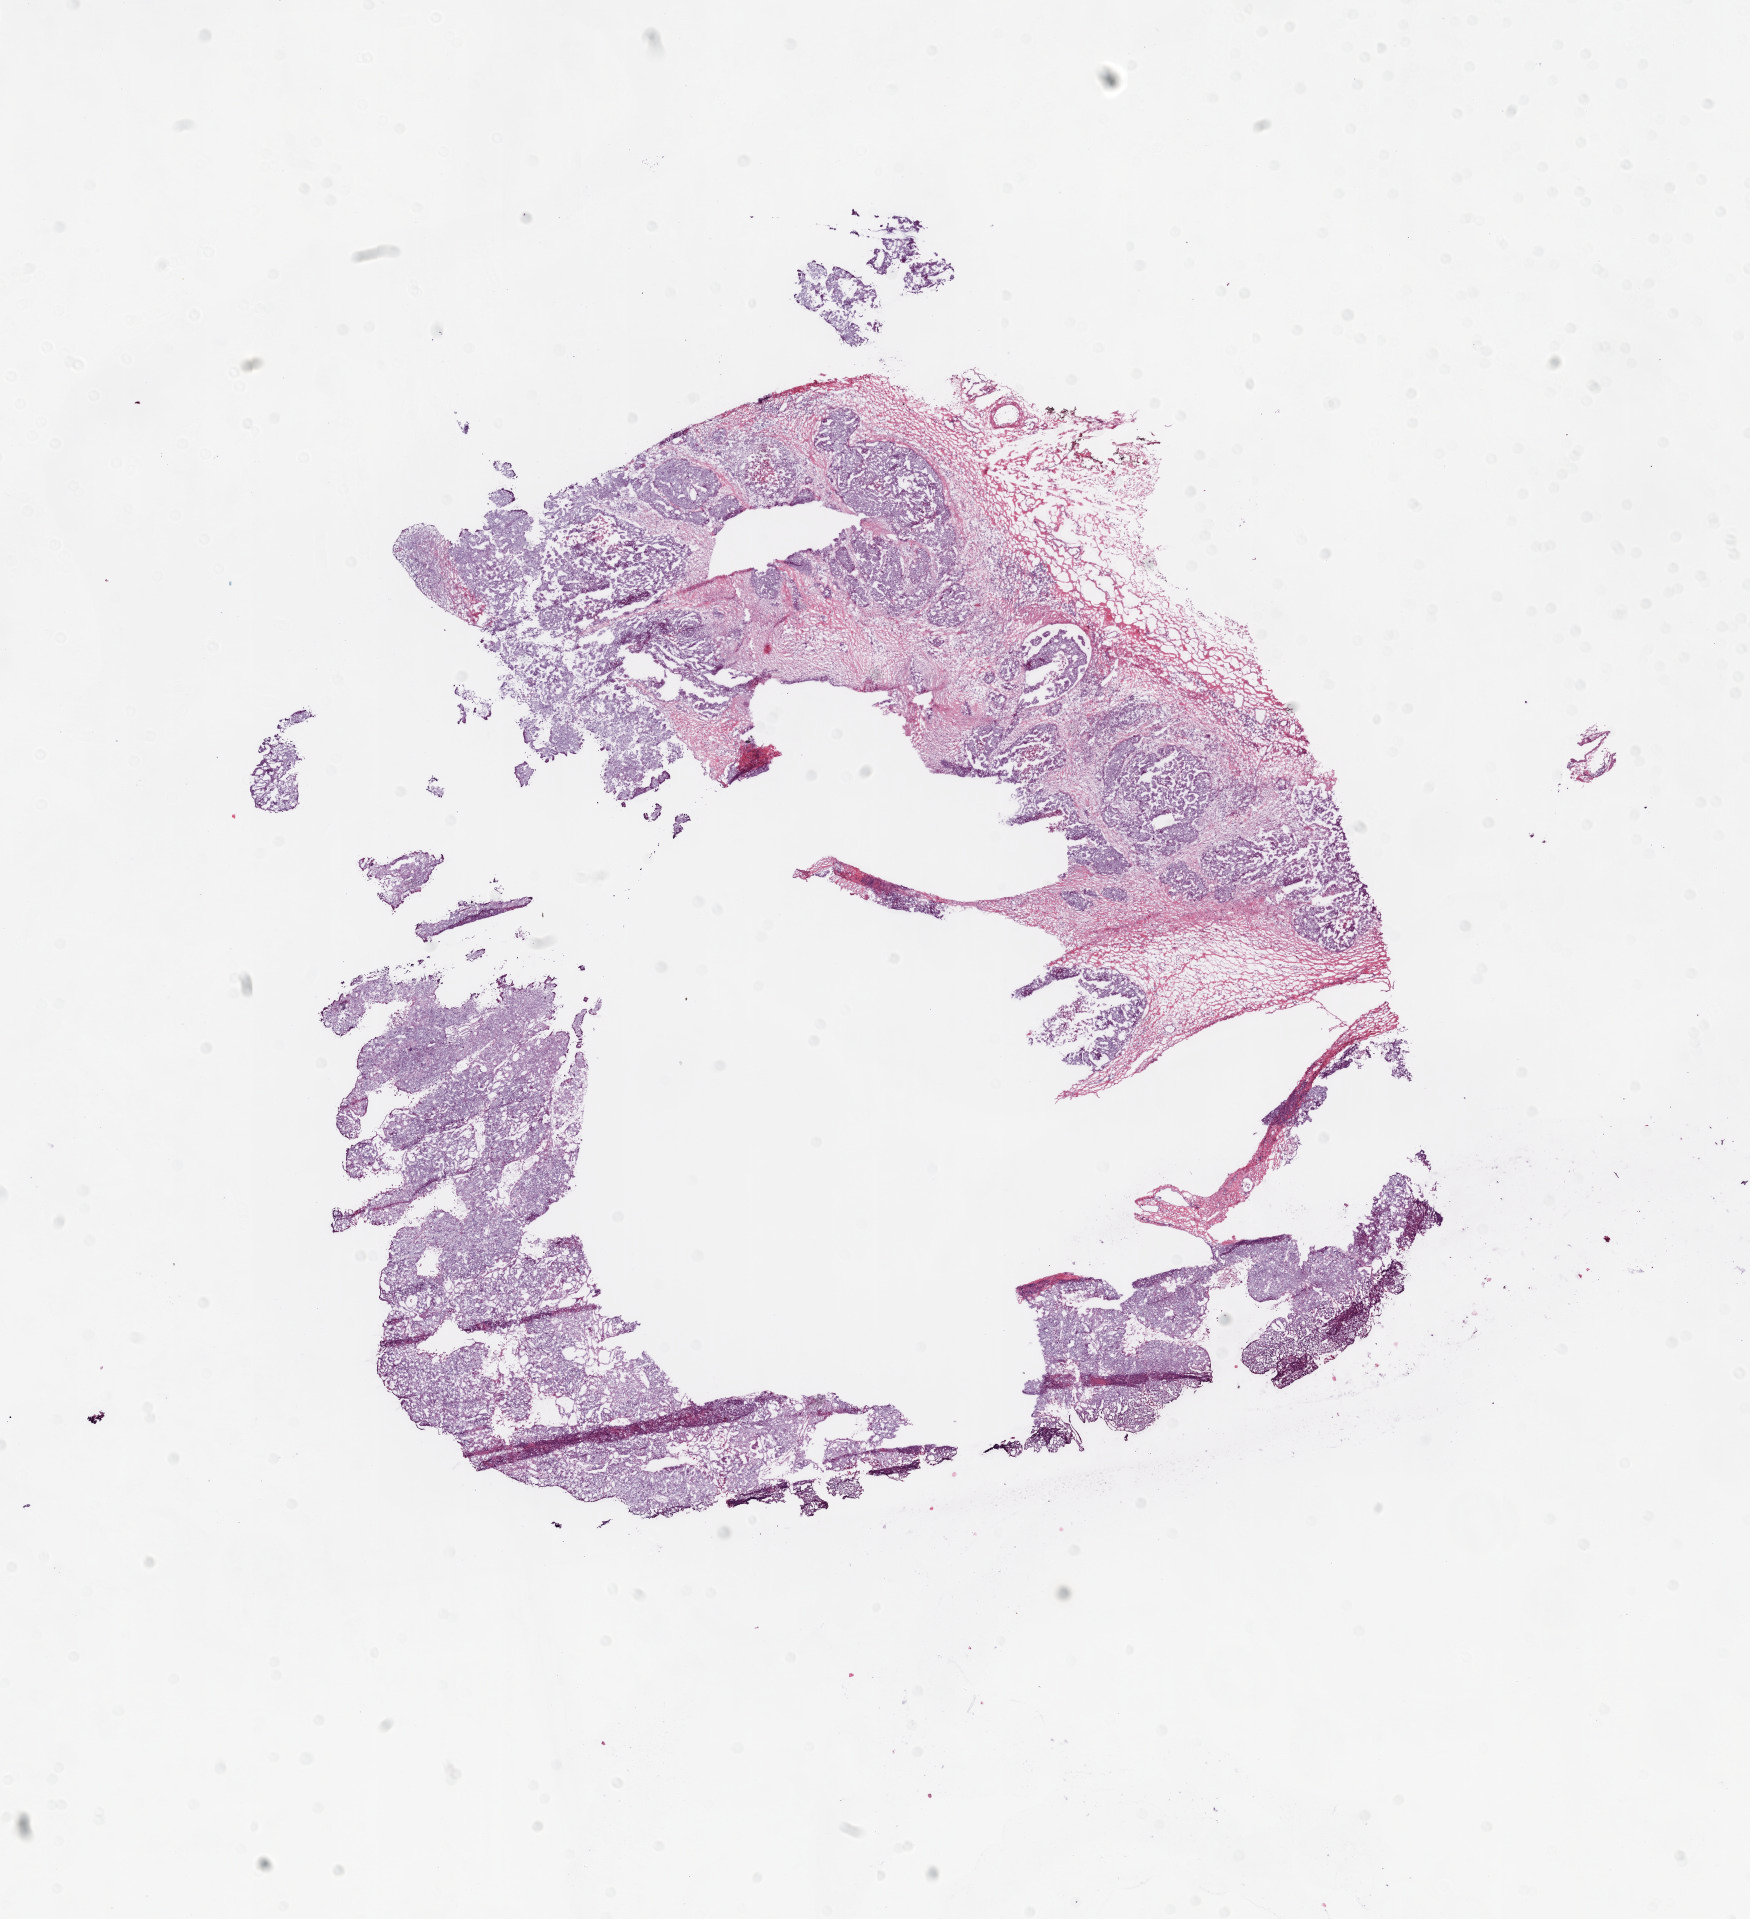
Whole-slide histology image, H&E-stained, low-resolution overview of the scanned area, about 14.0 x 15.4 mm (from a 20x scan), frozen section, primary tumour sample from the ovary. Female patient; age at initial diagnosis 56 years. Histologic grade: G3 (poorly differentiated). Slide review estimates, as recorded: tumour cells 89%, tumour nuclei 90%, normal cells 0%, stromal cells 10%, necrosis 1%.
Diagnosis: Serous cystadenocarcinoma, NOS. Laterality: bilateral. FIGO stage: IIIC.